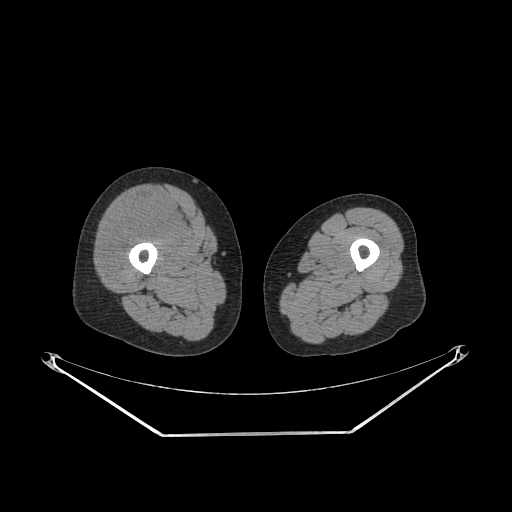
CT of an extremity soft-tissue mass (from a PET/CT study), one axial slice; 140 kVp; soft-tissue window (W 400 / L 40 HU); 3.75 mm slice thickness; 512 × 512 image matrix, field of view 500 × 500 mm. Female patient. Case-level facts recorded for this patient, not image findings: histological type: pleiomorphic undifferentiated sarcoma; grade: high; site of the primary tumour: right quadricep.
Annotated regions visible in this slice (expert contour drawn on MRI and transferred to this co-registered scan by the dataset authors):
- tumour plus oedema (research contour): box from (x=101, y=201) to (x=184, y=280) px
- tumour (research contour): (x=101, y=201)–(x=184, y=280)